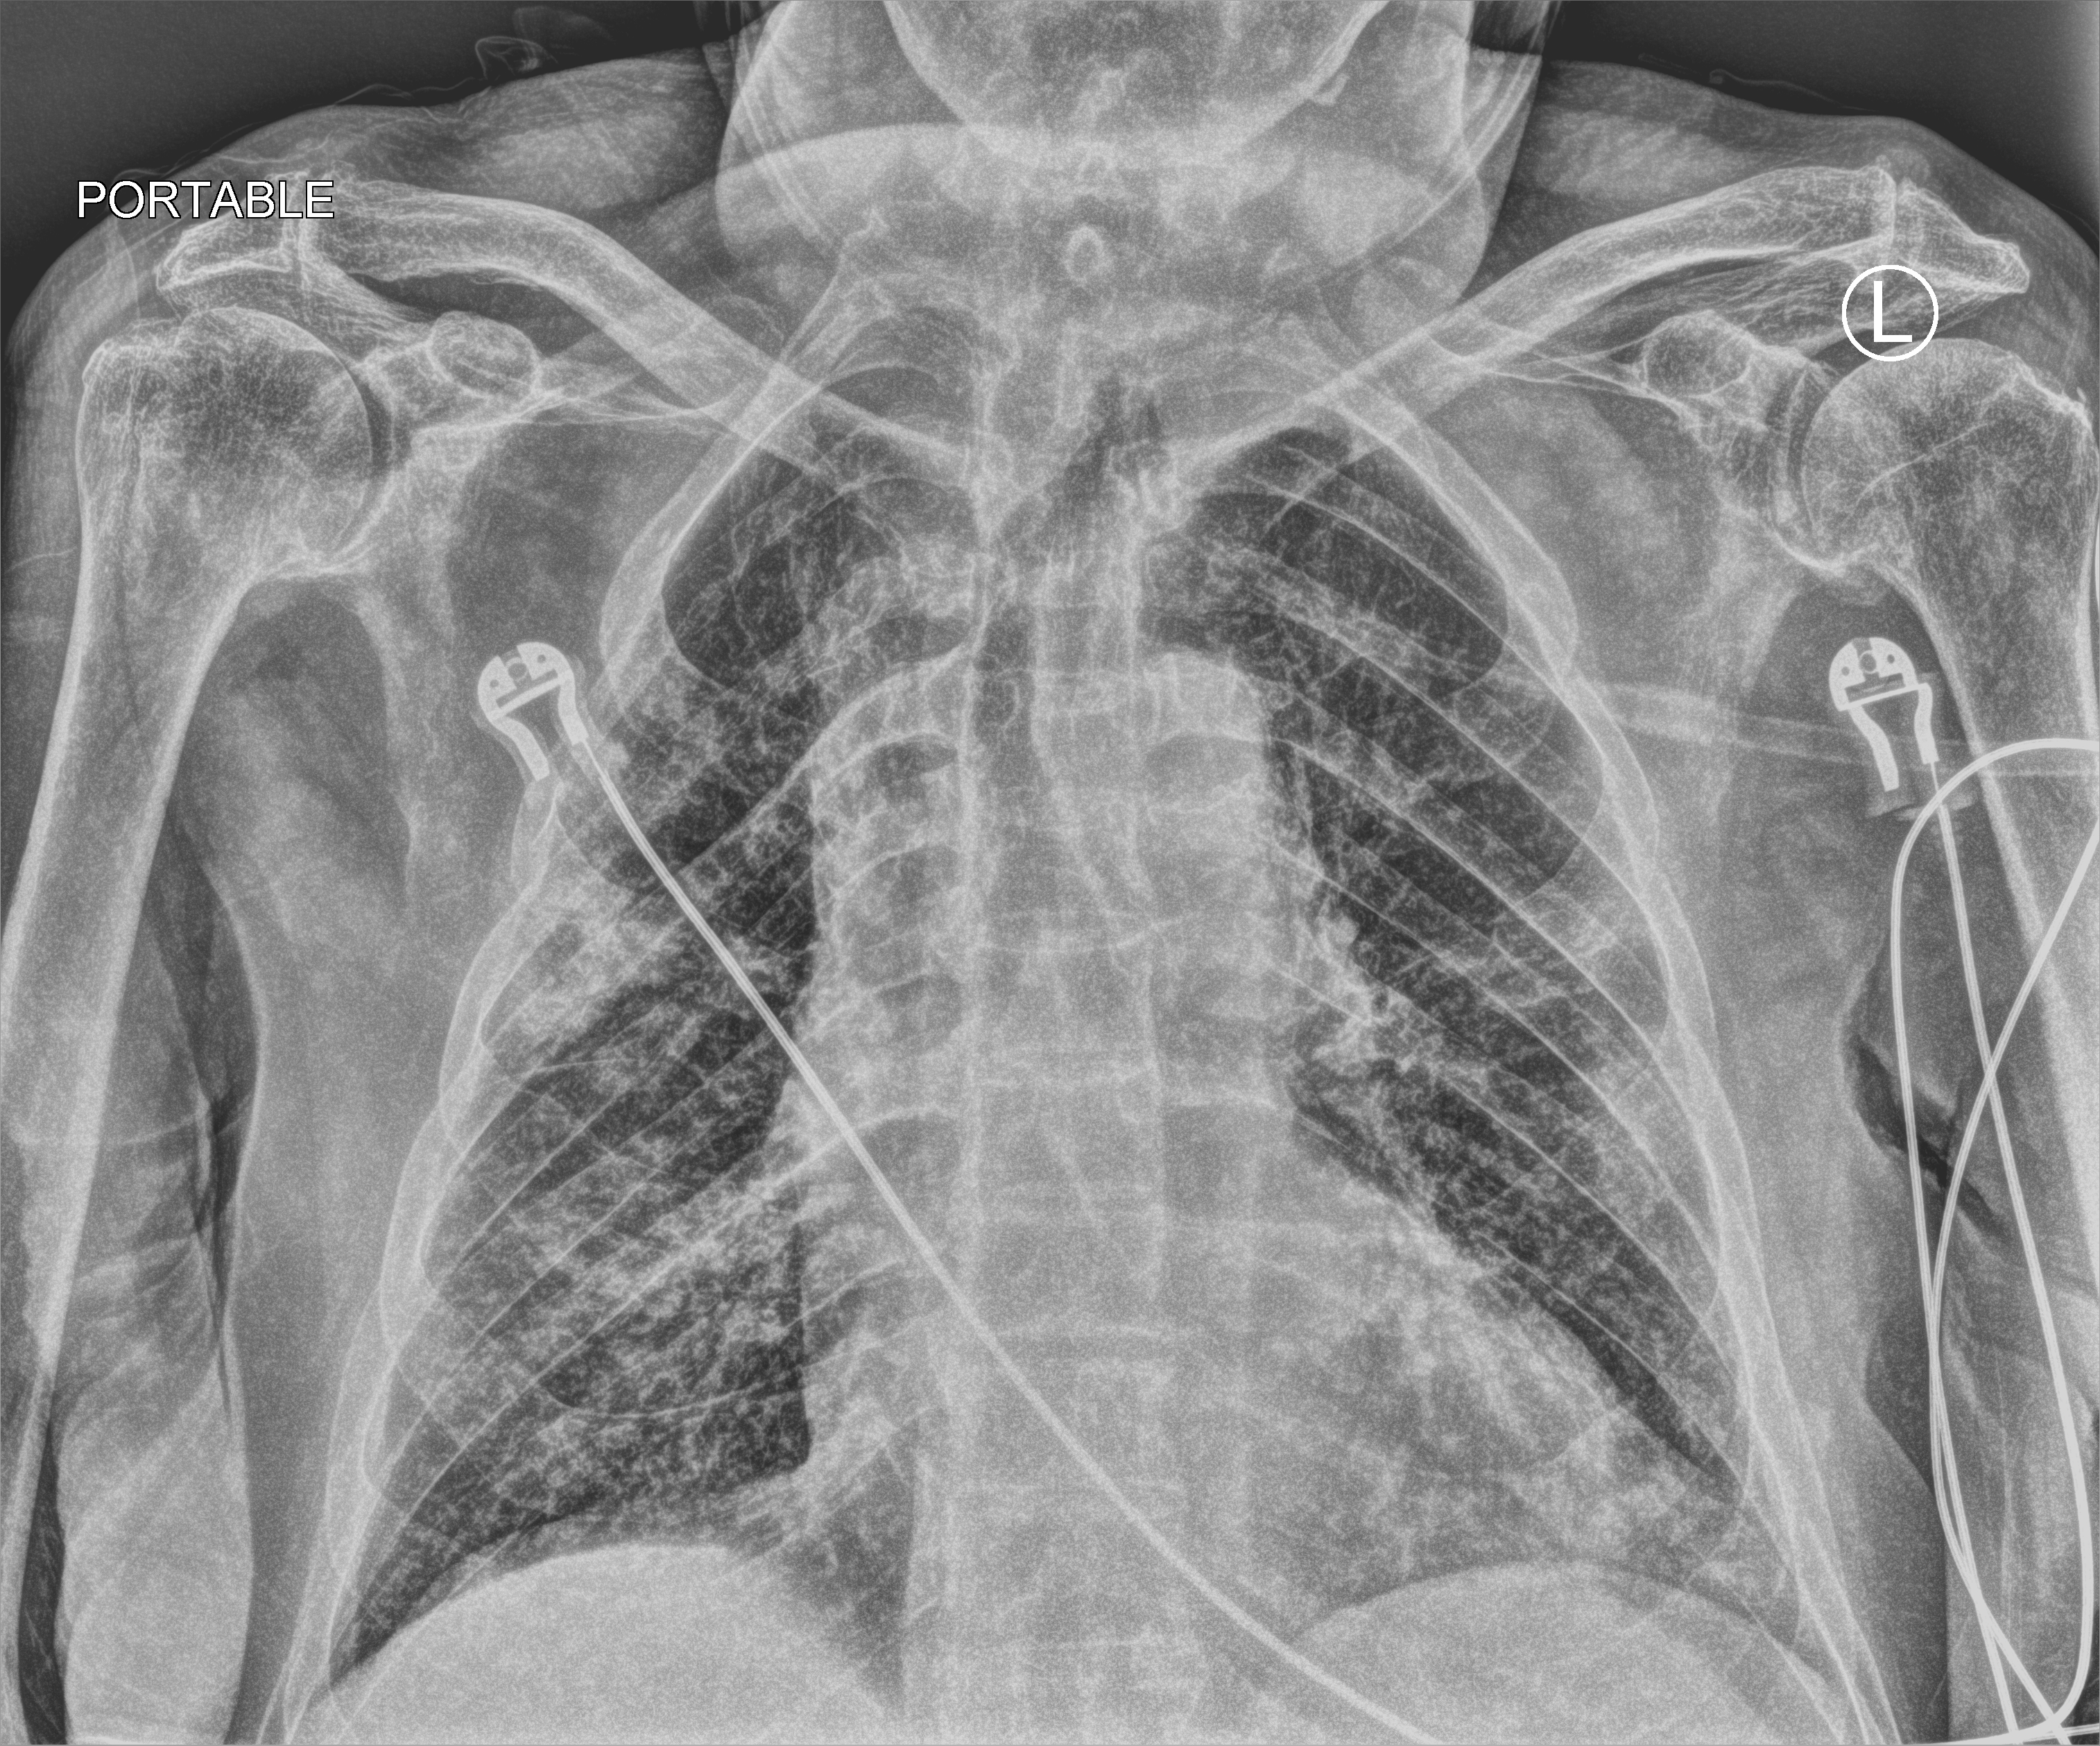
Portable chest radiograph, anteroposterior (AP) projection. Male patient hospitalised with COVID-19, age 75–90 years.
Hospital-stay facts (about this admission, not read from this image; timing relative to this image not recorded): hypertension (admission record): yes.